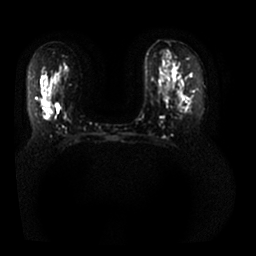
Breast MRI, one axial slice; slice 17 of 25 in the series (ordered by position); diffusion-weighted series; image 2 of 4 stored at this slice position (different b-values; order by instance number); 1.5 T; 4 mm slice thickness; 256 × 256 image matrix, field of view 350 × 350 mm. Female patient.
Structures marked on this image (outlined manually by an expert reader):
- tumour on diffusion-weighted imaging: bounding box <46,109,52,119> (left, top, right, bottom; pixels)